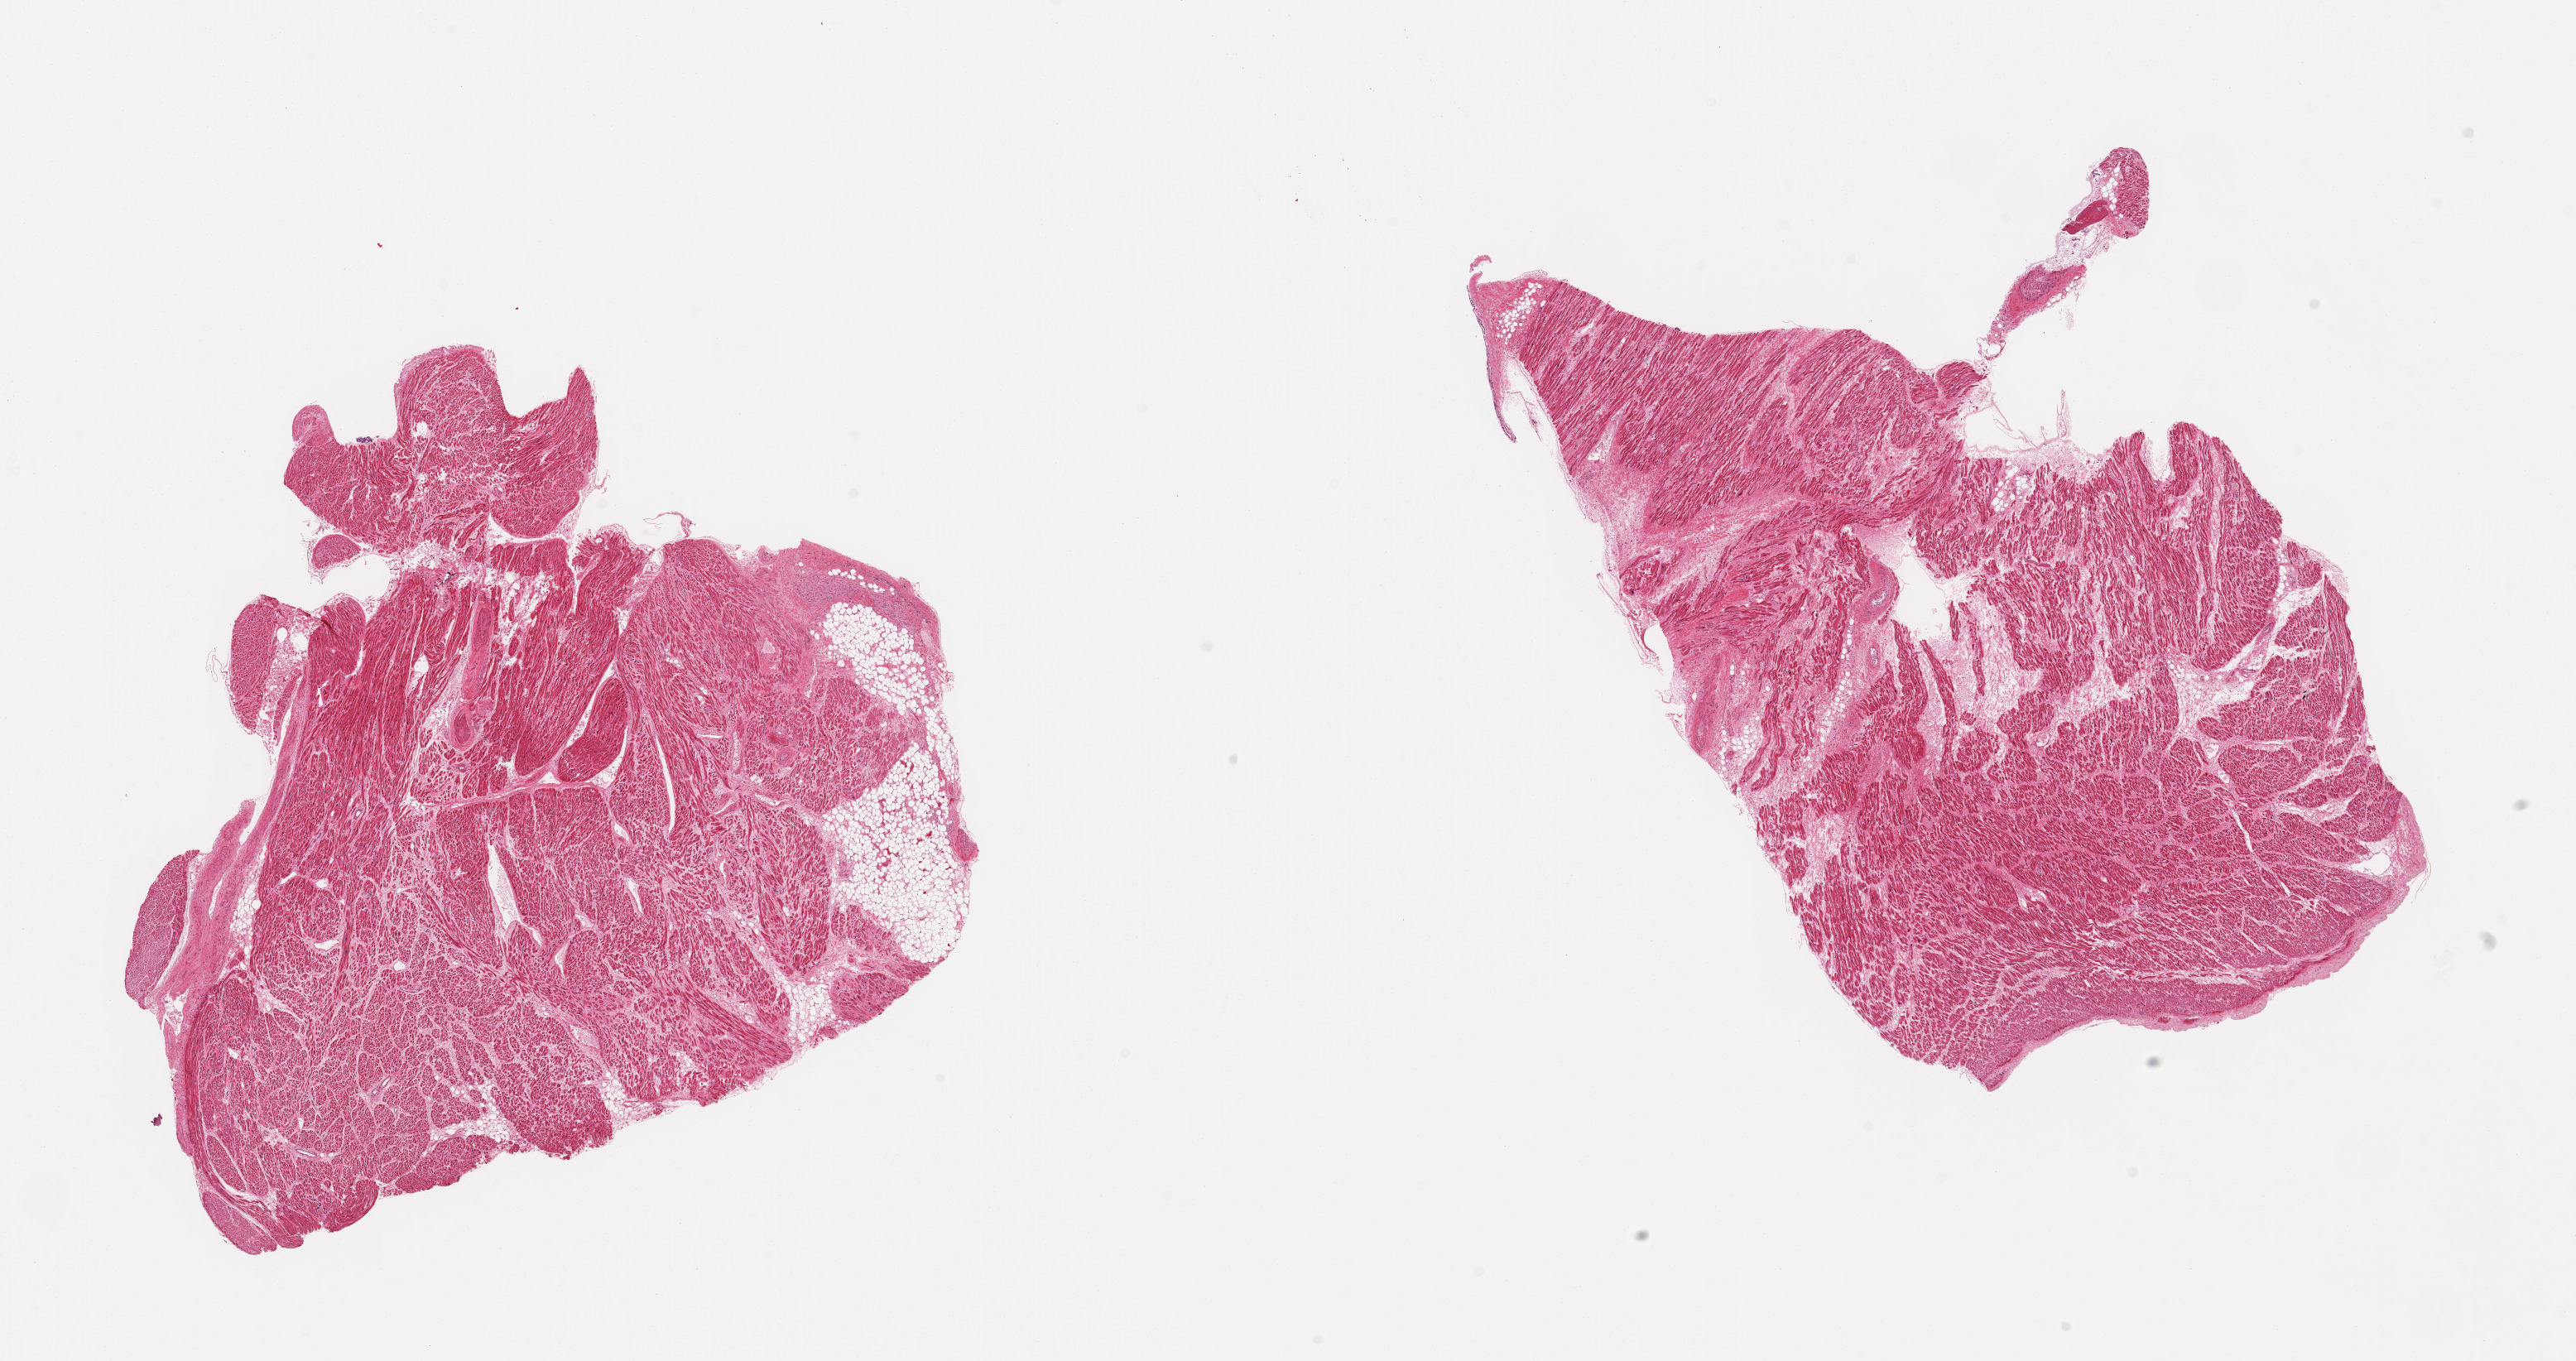
Whole-slide image, haematoxylin and eosin stain, brightfield — a low-resolution overview of the entire scanned area, about 24.6 x 13.0 mm (acquisition: 20x scan). PAXgene-fixed paraffin-embedded (PFPE) section. Sampled site (target tissue): auricular appendage. Donor tissue sample.
Reviewer comment on this tissue sample: 2 pieces, no abnormalities.